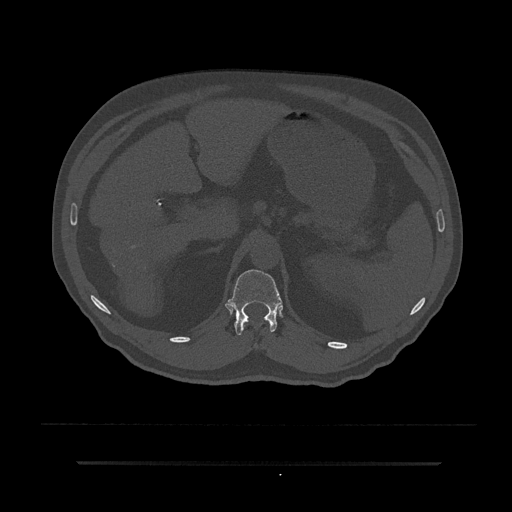
CT including the spine, one axial slice; position 223 of 797 along the scan axis; 120 kVp; bone window (W 1800 / L 400 HU); 0.5 mm slice thickness; 512 × 512 image matrix, field of view 464 × 464 mm. Male patient, age 59 years. From the clinical record (not read from this slice): primary cancer: bile ducts; vertebrae with lytic lesions (as recorded): T10.
Annotated regions visible in this slice (semi-automatic segmentation, software-assisted and operator-edited):
- T12 vertebra: box from (x=228, y=269) to (x=282, y=336) px